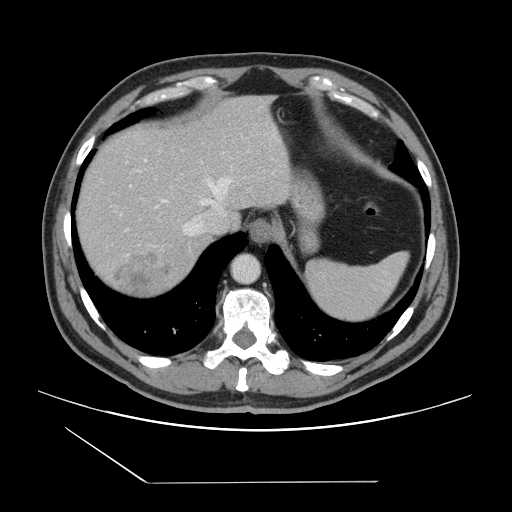
Contrast-enhanced abdominal CT, one axial slice. Position 122 of 157 along the scan axis. Intravenous contrast given. Soft-tissue window (W 400 / L 40 HU). 512 × 512 image matrix, field of view 407 × 407 mm. Male patient, age 61 years. Case-level facts recorded for this patient, not image findings: diagnosis: colorectal cancer liver metastases, imaged before liver resection; multiple liver metastases: yes; largest metastasis: 5.5 cm; disease in both lobes: yes.
Outlined on this slice (outlined manually by an expert reader):
- hepatic veins: box from (x=162, y=178) to (x=232, y=236) px
- liver: (x=75, y=96)–(x=291, y=300)
- planned liver remnant (the part of the liver to remain after resection): (x=76, y=101)–(x=234, y=229)
- liver metastasis: (x=110, y=250)–(x=177, y=298)